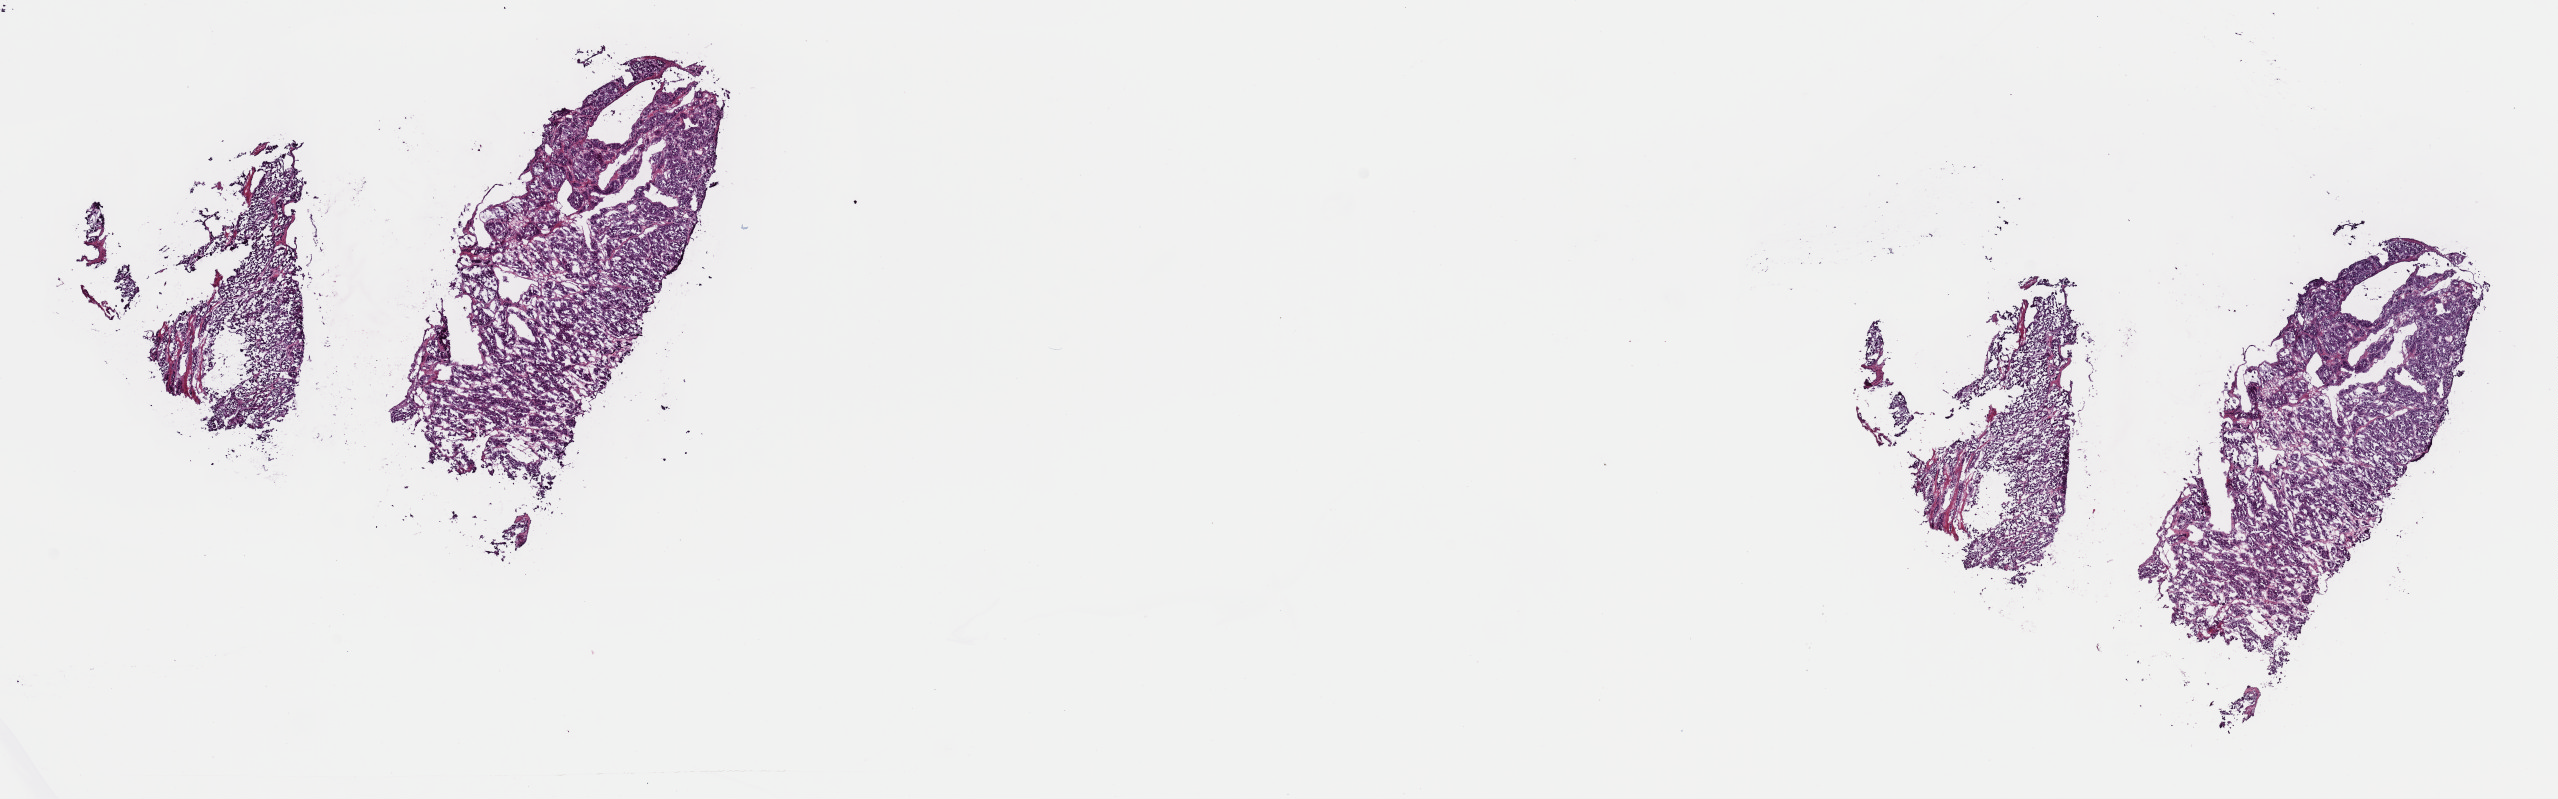
Whole-slide histology image, H&E — low-resolution overview of the scanned area, about 20.2 x 6.3 mm (slide scanned at 40x). Frozen section. Sample: primary tumour, adrenal cortex. Female patient; age at initial diagnosis 69 years. Slide review estimates, as recorded: tumour cells 100%, tumour nuclei 95%, normal cells 0%, stromal cells 0%, necrosis 0%. Infiltration values recorded for this section: lymphocyte infiltration 0%, monocyte infiltration 0%, neutrophil infiltration 0%.
- histologic diagnosis: Adrenal cortical carcinoma (cortex of adrenal gland)
- laterality: left